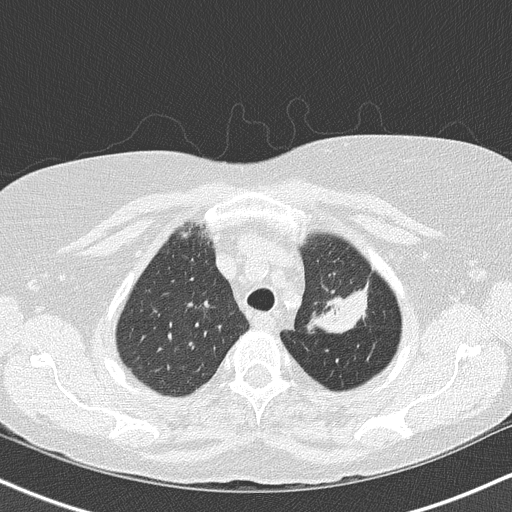
Low-dose screening chest CT, axial slice, third screening round (two years after baseline), lung window (W 1500 / L -600 HU), slice 123 of 147 in the series. Female, age 68 years at enrolment. Former smoker at enrolment.
Expert reader's lesion annotation, box from (x=291, y=232) to (x=380, y=339) px. Reader record for this screening exam (exam-level; its link to the box is not recorded): non-calcified nodule or mass ≥4 mm, left upper lobe, 5 × 5 mm, poorly defined margins, mixed attenuation, pre-existing on the prior screen: yes; interval growth: yes. Official screen result: positive, other. Participant outcome: lung cancer diagnosed 42 days after this screen — adenocarcinoma, NOS, left upper lobe, poorly differentiated (G3), stage IB (AJCC 6th edition), 50 mm at pathology.